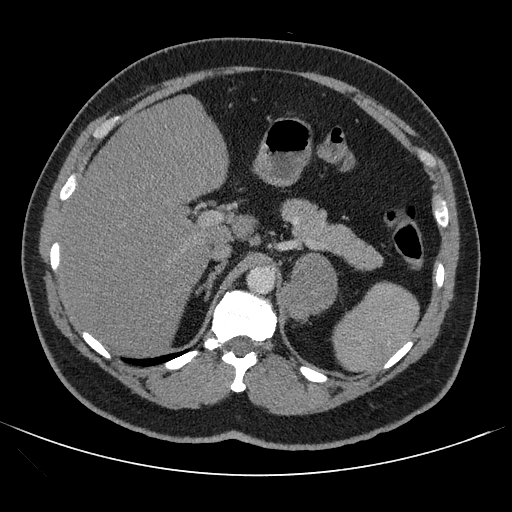
Contrast-enhanced abdominal CT, one axial slice. 120 kVp. Intravenous contrast given. Soft-tissue window (W 400 / L 40 HU). 2.5 mm slice thickness. 512 × 512 image matrix, field of view 399 × 399 mm. Male patient, age 53 years. Case-level facts recorded for this patient, not image findings: diagnosis: adrenocortical carcinoma; tumour side: left adrenal.
Annotated regions visible in this slice (semi-automatic segmentation, software-assisted and operator-edited):
- mass: bounding box <282,253,336,318> (left, top, right, bottom; pixels)